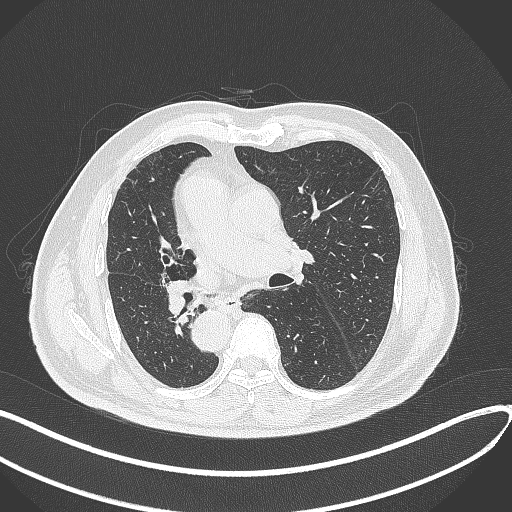
Chest CT, one axial slice. Position 154 of 300 along the scan axis. Lung window (W 1500 / L -600 HU). 512 × 512 image matrix, field of view 400 × 400 mm. Male patient, age 67 years. Case-level facts recorded for this patient, not image findings: clinical TNM (as recorded): T2a N0 M0.
Outlined on this slice (rectangle marked by the reading radiologist):
- lung tumour (recorded histology: squamous cell carcinoma): bounding box [x1, y1, x2, y2] px = [162, 275, 197, 321]